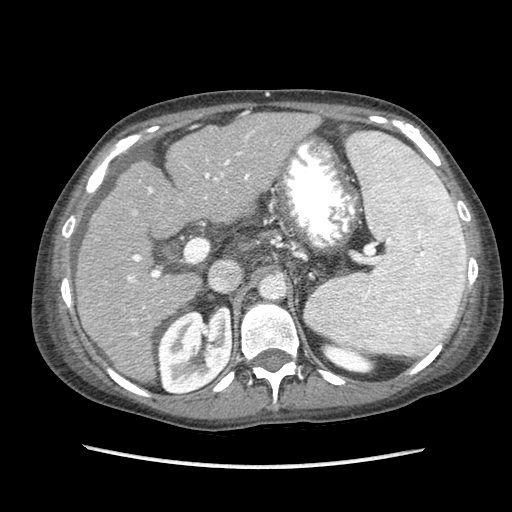
Contrast-enhanced abdominal CT (liver protocol), one axial slice; position 50 of 87 along the scan axis; reconstruction kernel STANDARD; soft-tissue window (W 400 / L 40 HU); 512 × 512 image matrix, field of view 340 × 340 mm. From the clinical record (not read from this slice): diagnosis: hepatocellular carcinoma (patient treated with transarterial chemoembolisation; whether this scan precedes or follows treatment is not stated here); TNM stage (as recorded): Stage-IIIB; Child-Pugh class: A; tumour nodularity: uninodular.
Structures marked on this image (semi-automatic segmentation, software-assisted and operator-edited):
- liver parenchyma outside the tumour (the mass and vessels are separate outlines, so this box may not span the whole liver): box from (x=76, y=112) to (x=320, y=382) px
- liver vessels: (x=127, y=113)–(x=254, y=335)